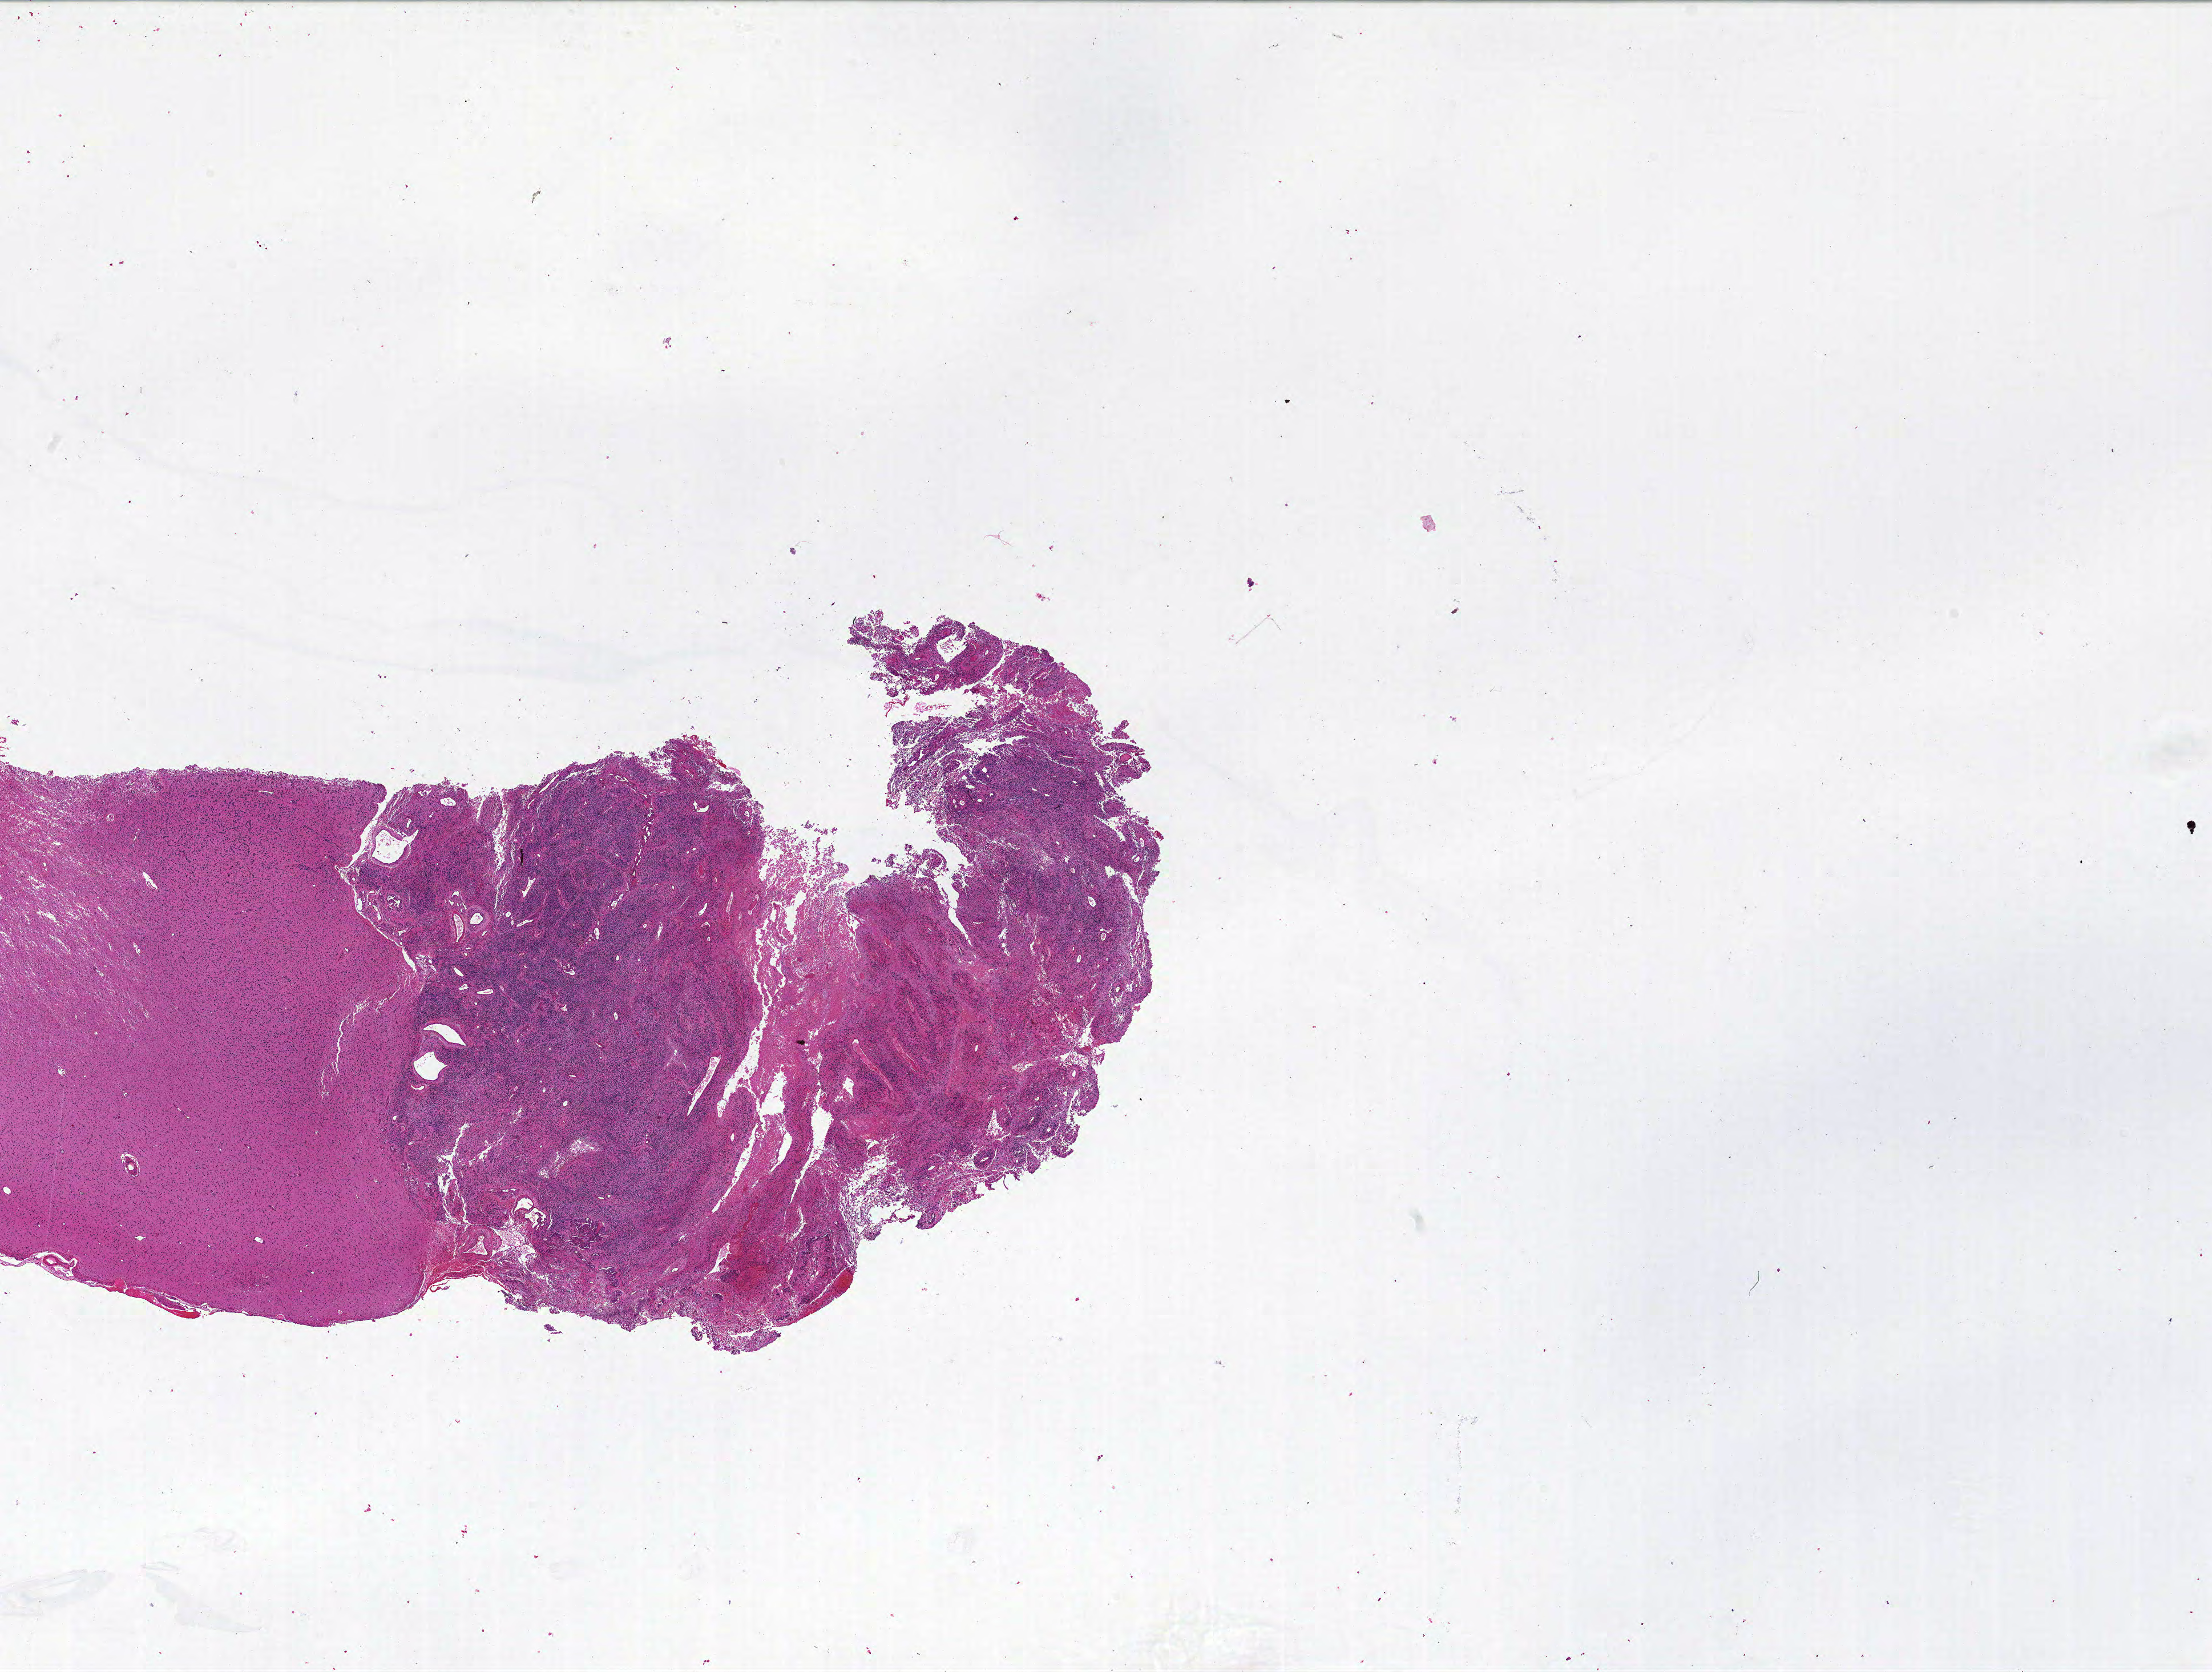
Digitized H&E tissue section (whole slide) — low-resolution overview of the scanned area, about 31.0 x 23.4 mm (acquisition: 20x scan), formalin-fixed paraffin-embedded (FFPE) diagnostic section, brain, primary tumour sample. Patient: male, age at initial diagnosis 62 years.
Diagnosis: Glioblastoma.